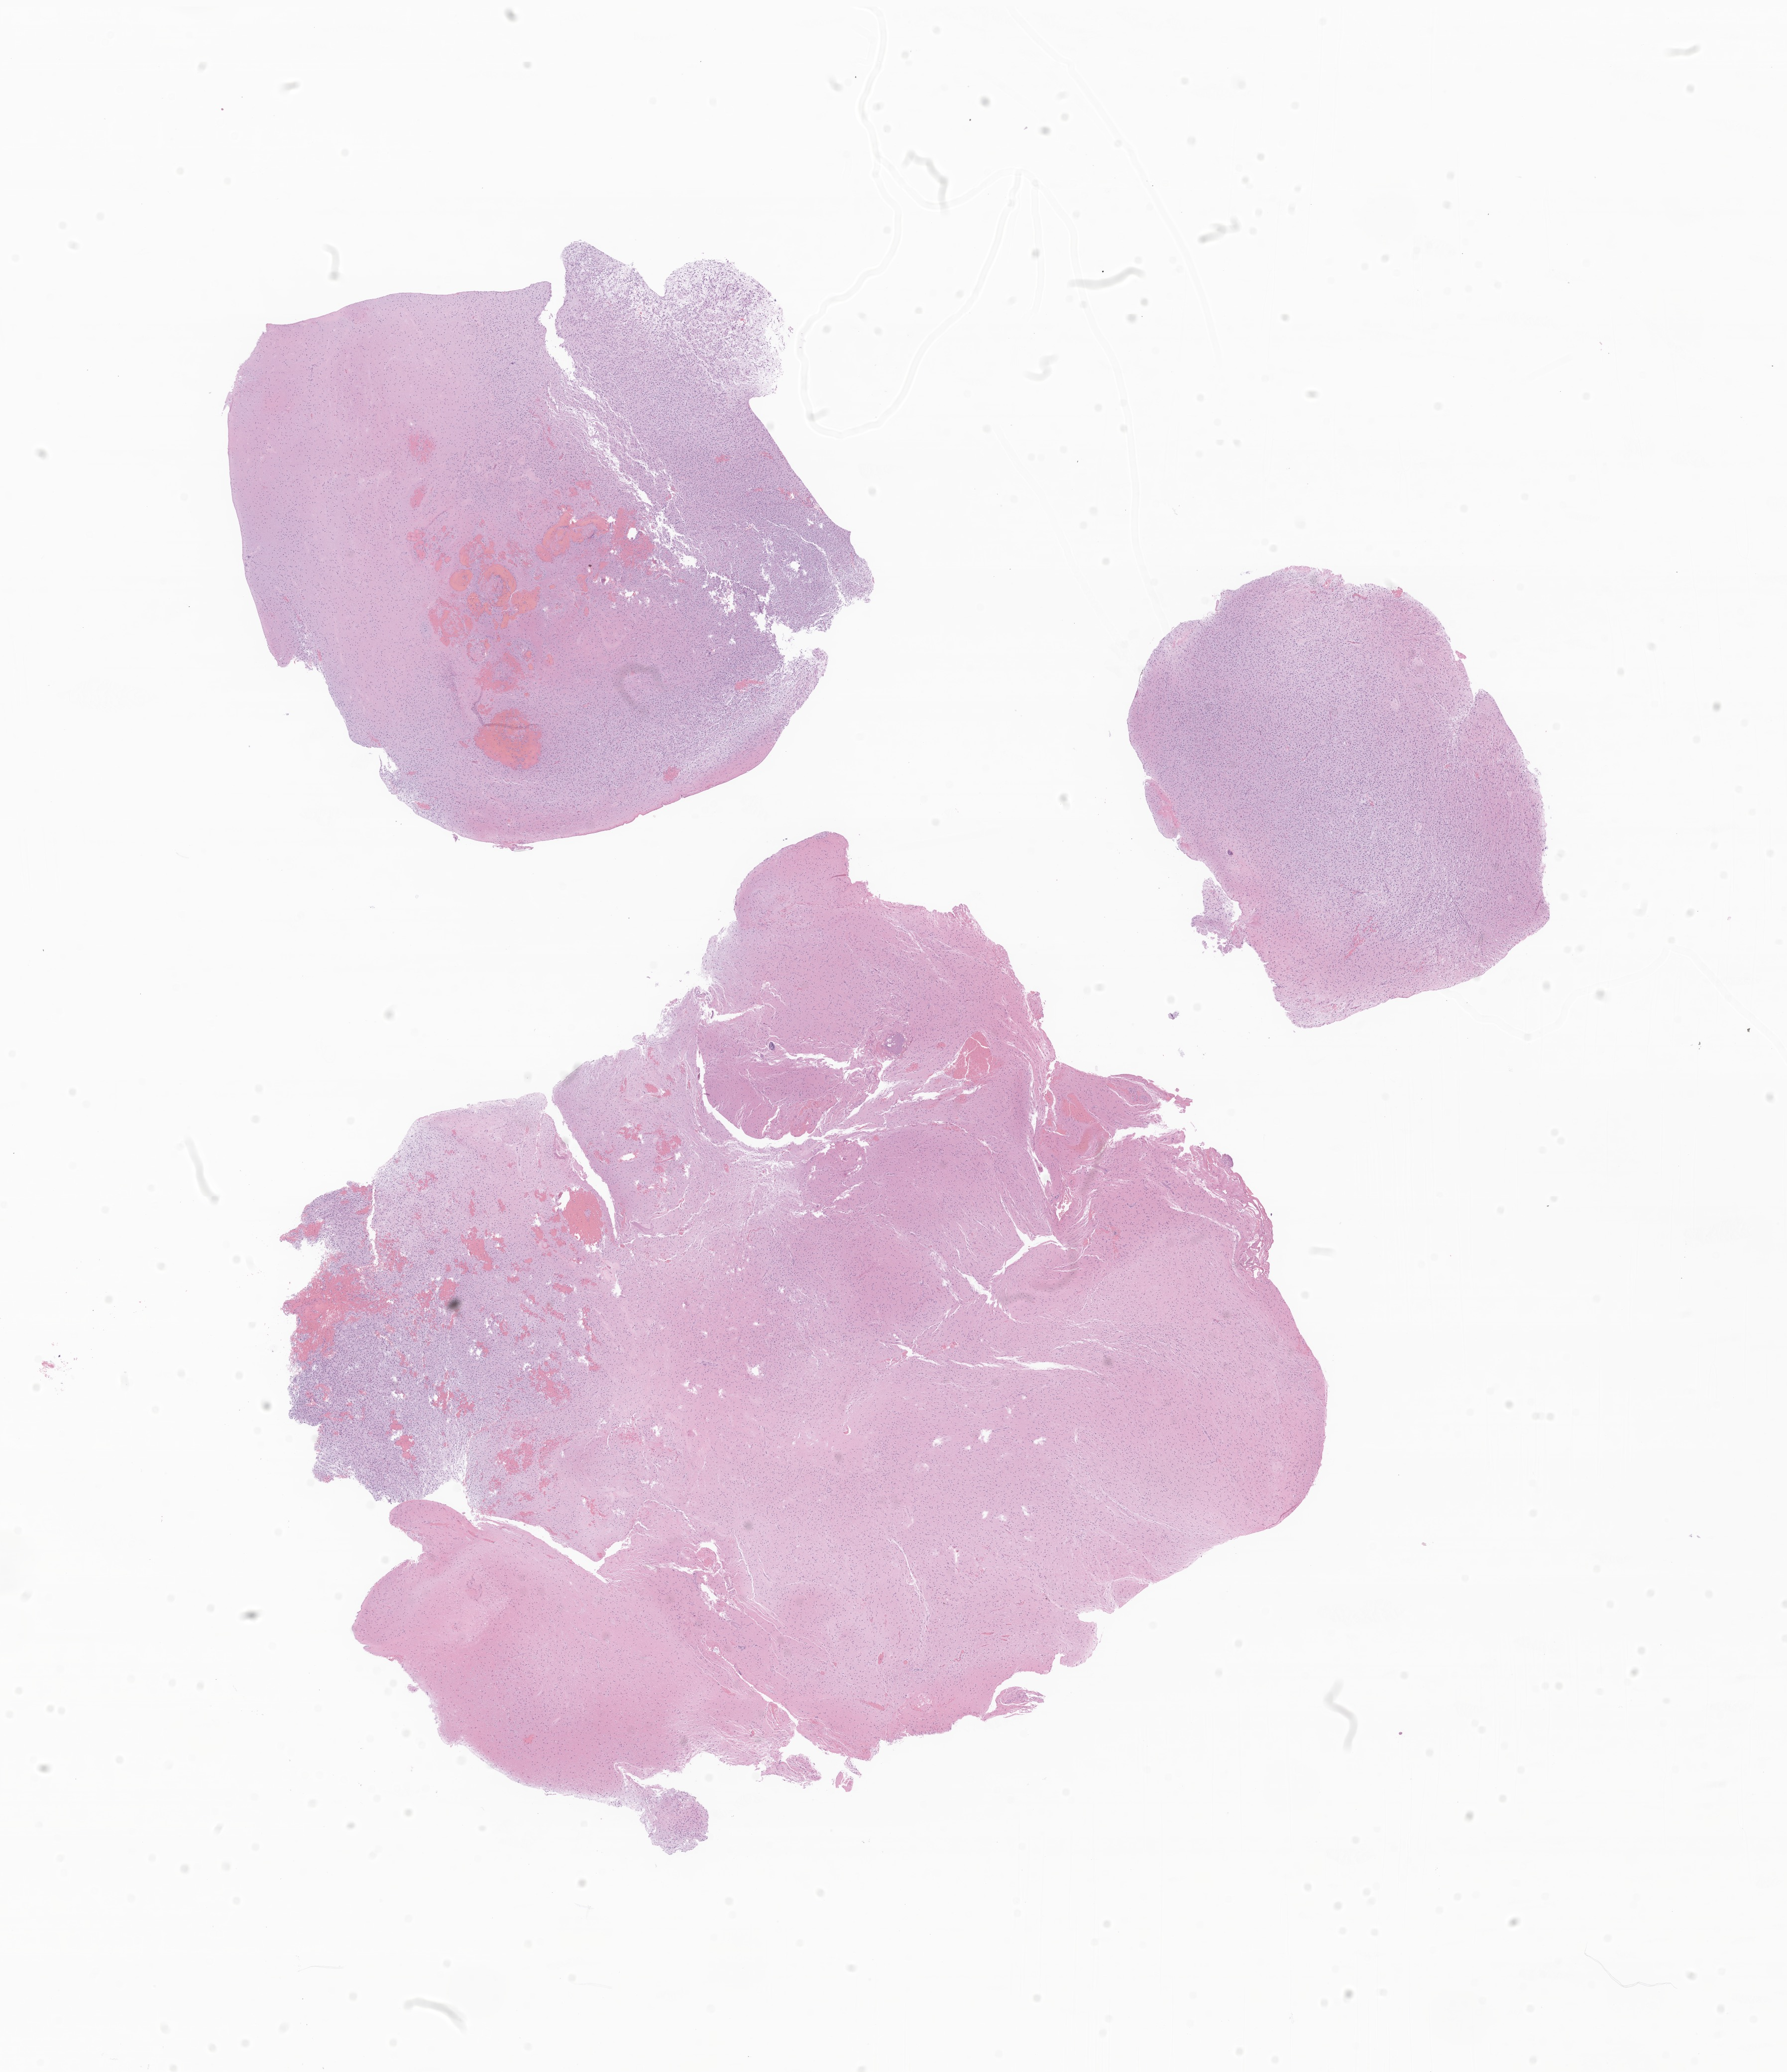
Hematoxylin and eosin (H&E) whole-slide image of tumor tissue from the brain — low-resolution overview of the scanned area, about 15.1 x 17.5 mm; FFPE section. Patient: male, age 173 months.
Diagnosis: Neoplasm, uncertain whether benign or malignant.